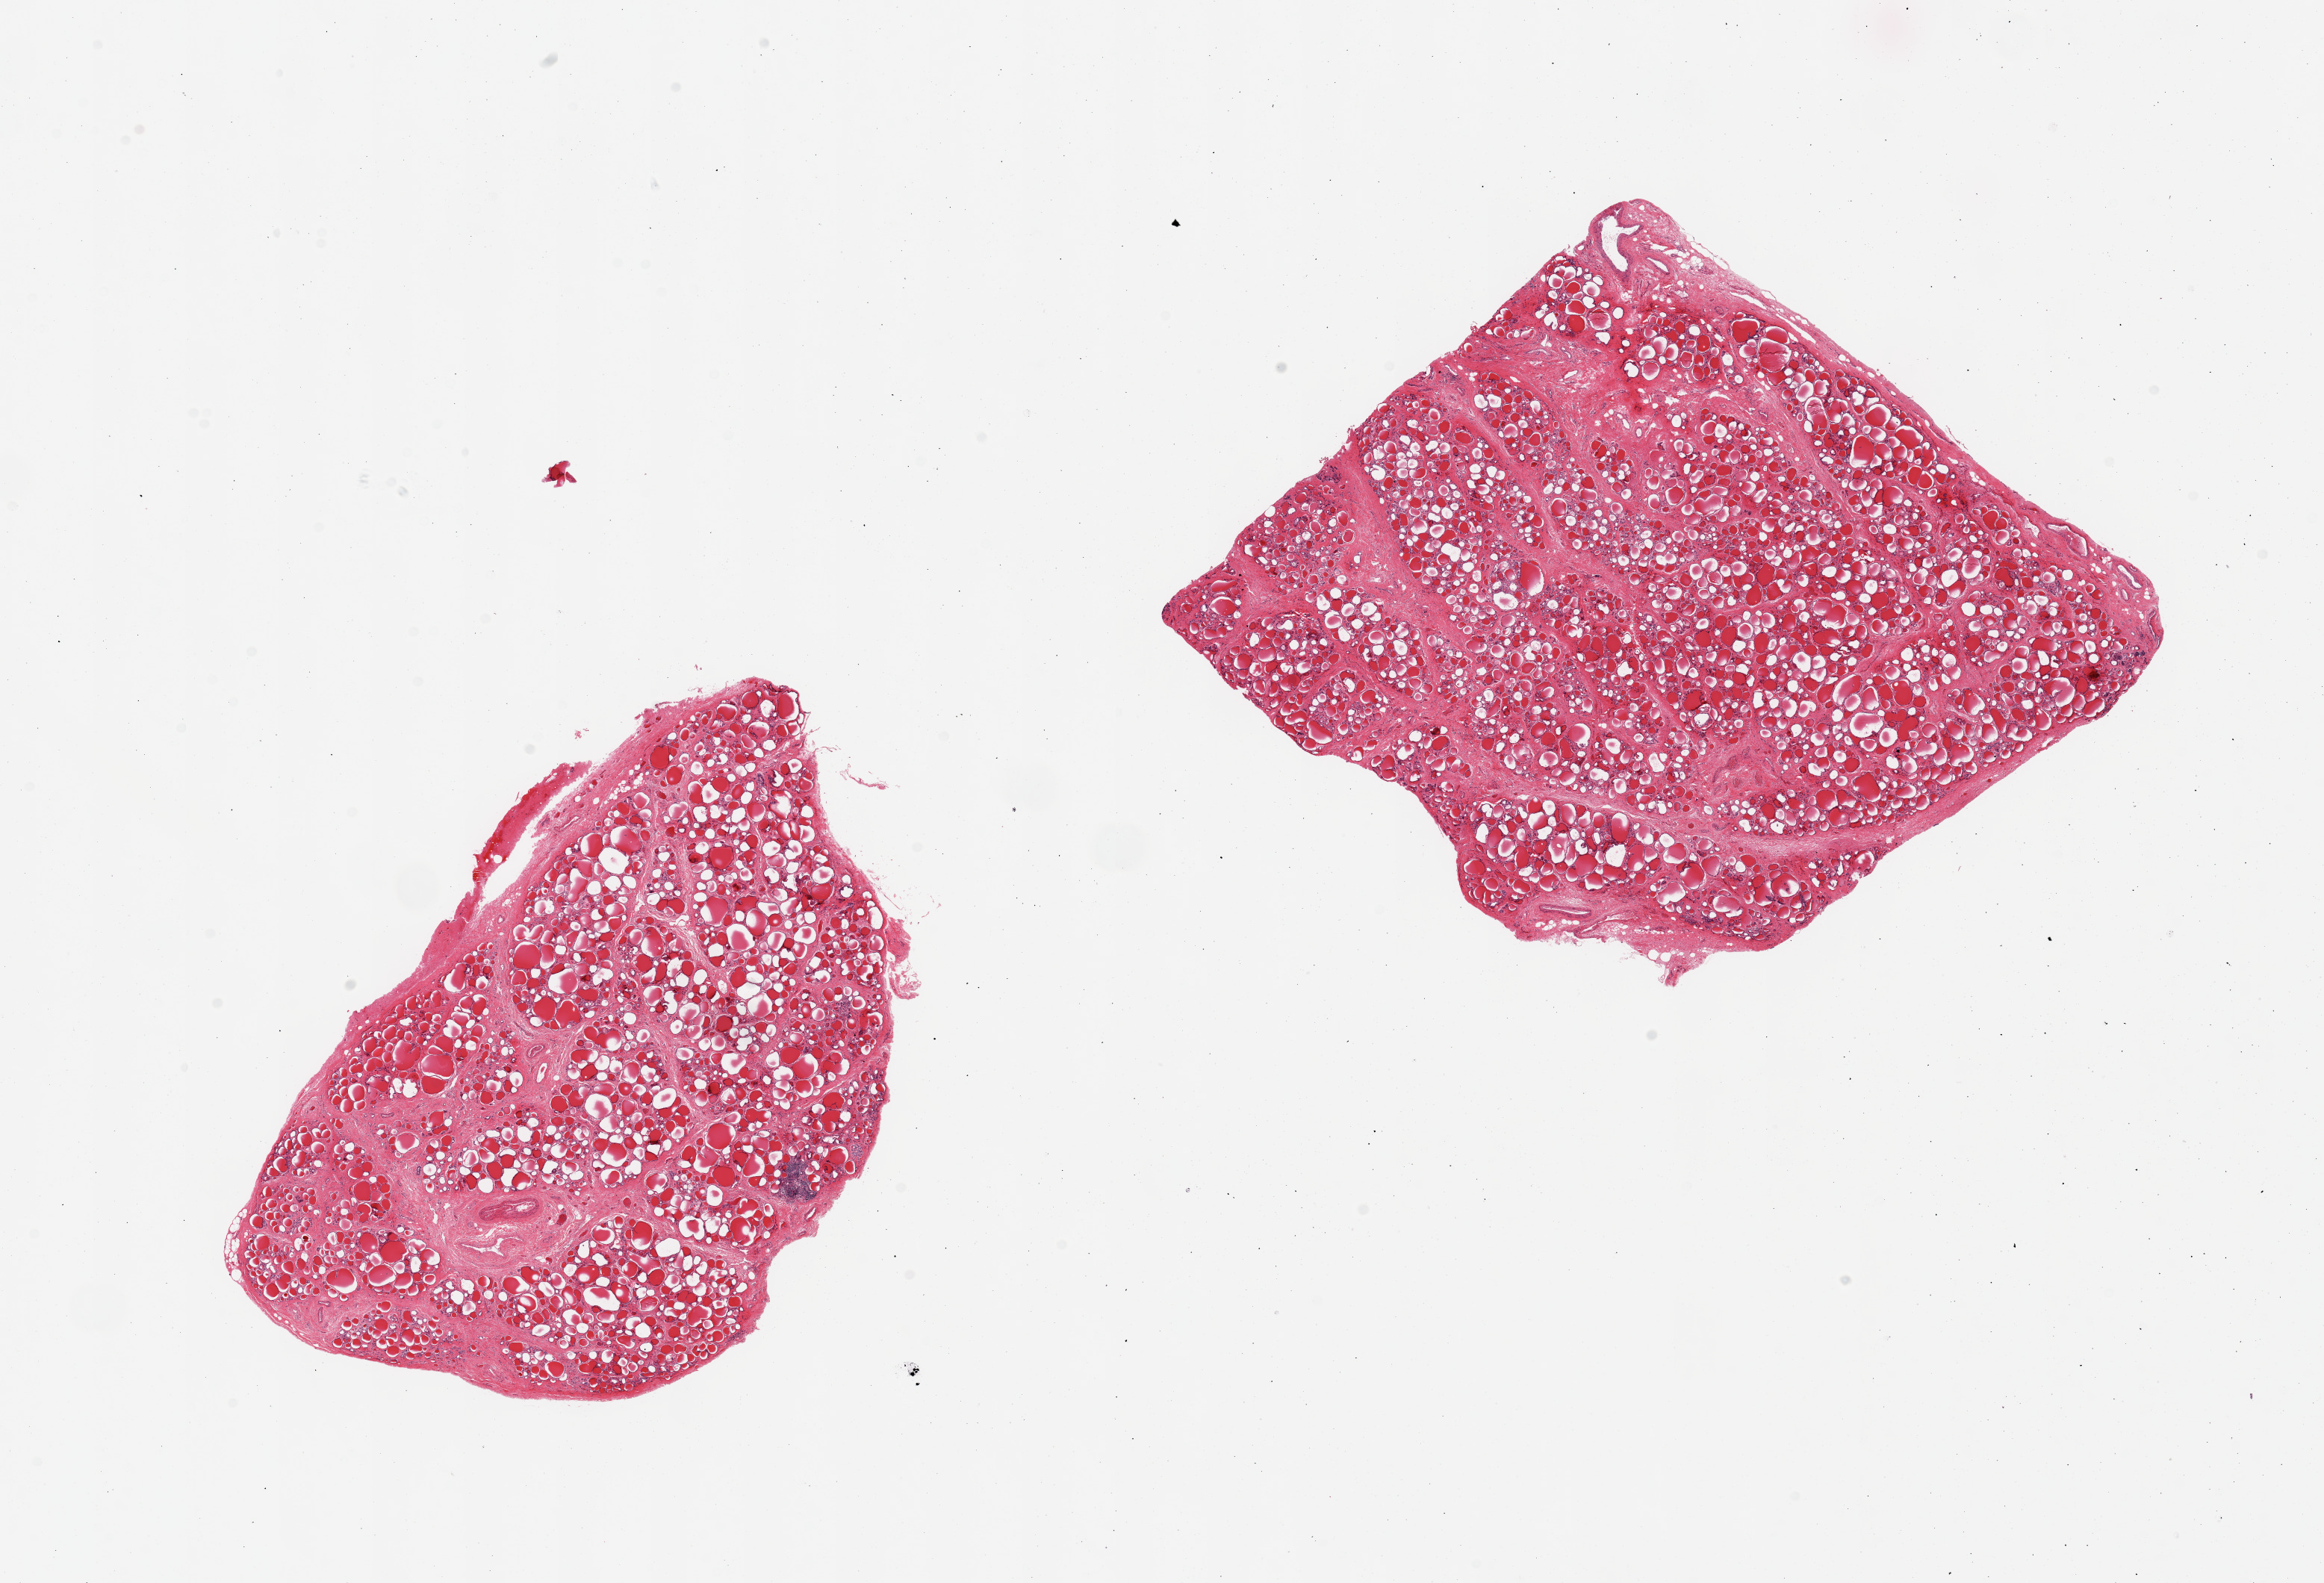
Hematoxylin and eosin (H&E) whole-slide image — low-resolution overview of the scanned area, about 24.6 x 16.8 mm (from a 20x scan); PAXgene-fixed, paraffin-embedded tissue; sampled site (target tissue): thyroid; tissue donor sample. Male donor.
Pathologist's review note for this sample: 2 piecesm features of goiter; prominent regressive changes/scarring.